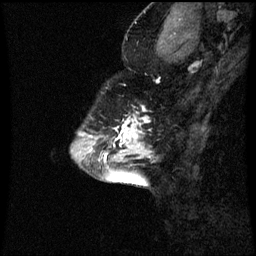
Breast MRI (dynamic contrast-enhanced), one sagittal slice. Position 21 of 60 along the scan axis. Dynamic contrast-enhanced series, image 2 of 3 at this slice position (ordered by acquisition). 1.5 T. TE 4.2 ms, TR 8.9 ms. 2 mm slice thickness. 256 × 256 image matrix. Patient: female, 43 years. From the clinical record (not read from this slice): setting: breast cancer imaged before/during neoadjuvant chemotherapy; receptor status: HR-positive, HER2-negative.
Structures marked on this image (semi-automatically segmented with operator editing):
- analysis volume of interest (the breast-tissue region the enhancement analysis was run in; not a lesion): bounding box [x1, y1, x2, y2] px = [96, 106, 153, 159]
- tumour enhancement mask (voxels above the 70 % enhancement threshold inside the analysis volume of interest): [104, 108, 149, 159]